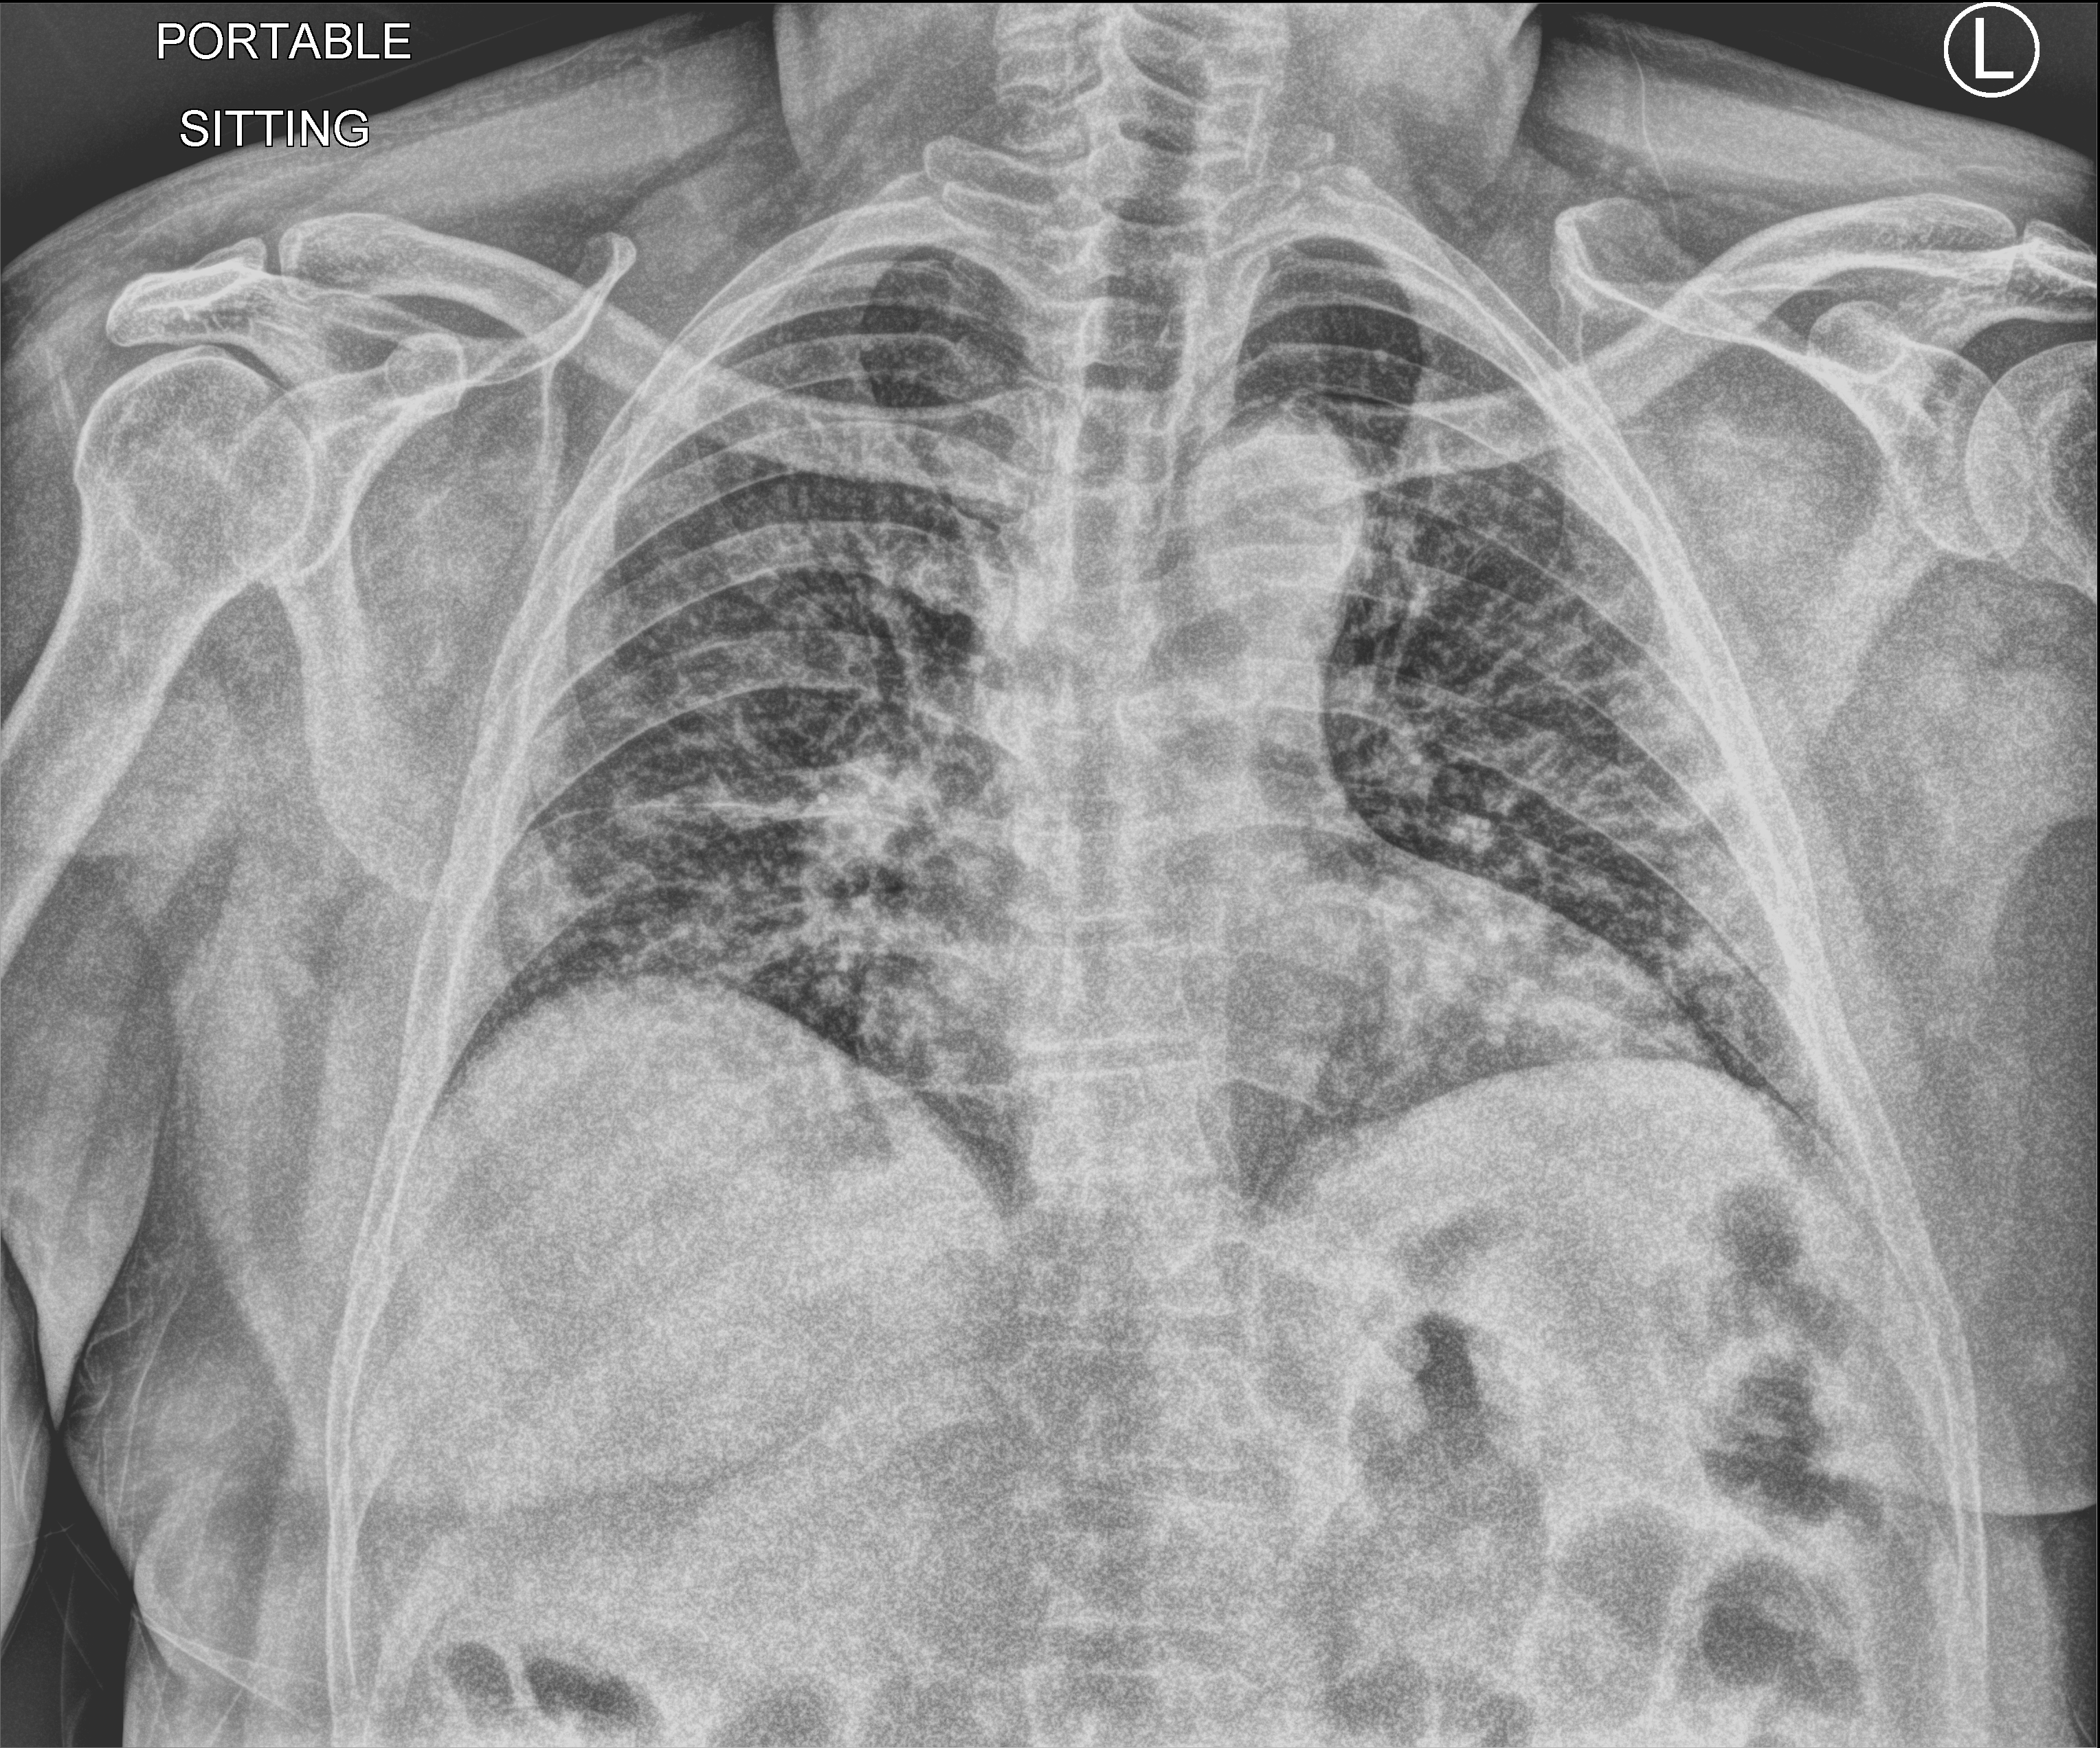
Chest X-ray (portable), anteroposterior (AP) projection. Male patient hospitalised with COVID-19, age 18–59 years.
Admission-level facts for this patient (not findings on this image; timing relative to this image not recorded):
- admitted to intensive care during this hospital stay: no